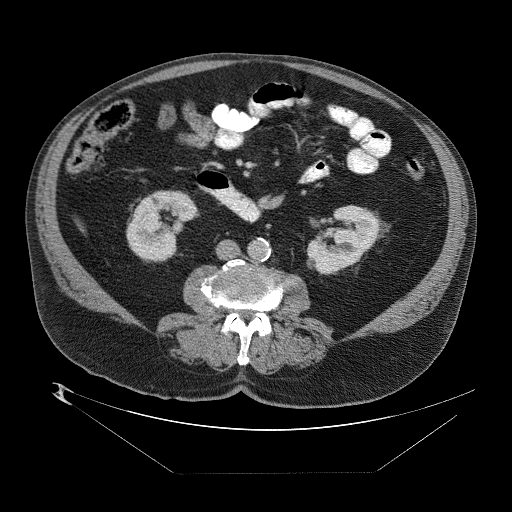
Contrast-enhanced abdominal CT (liver protocol), one axial slice; slice 1 of 89 in the series (ordered by position); one of 2 acquisitions stored at this slice position; soft-tissue window (W 400 / L 40 HU); 2.5 mm slice thickness; 512 × 512 image matrix. From the clinical record (not read from this slice): diagnosis: hepatocellular carcinoma (patient treated with transarterial chemoembolisation; whether this scan precedes or follows treatment is not stated here); TNM stage (as recorded): Stage-II; Child-Pugh class: B; tumour size: 4 cm.
Annotated regions visible in this slice (semi-automatic segmentation, software-assisted and operator-edited):
- abdominal aorta: box from (x=249, y=238) to (x=272, y=262) px
- liver parenchyma outside the tumour (the mass and vessels are separate outlines, so this box may not span the whole liver): (x=78, y=218)–(x=84, y=228)